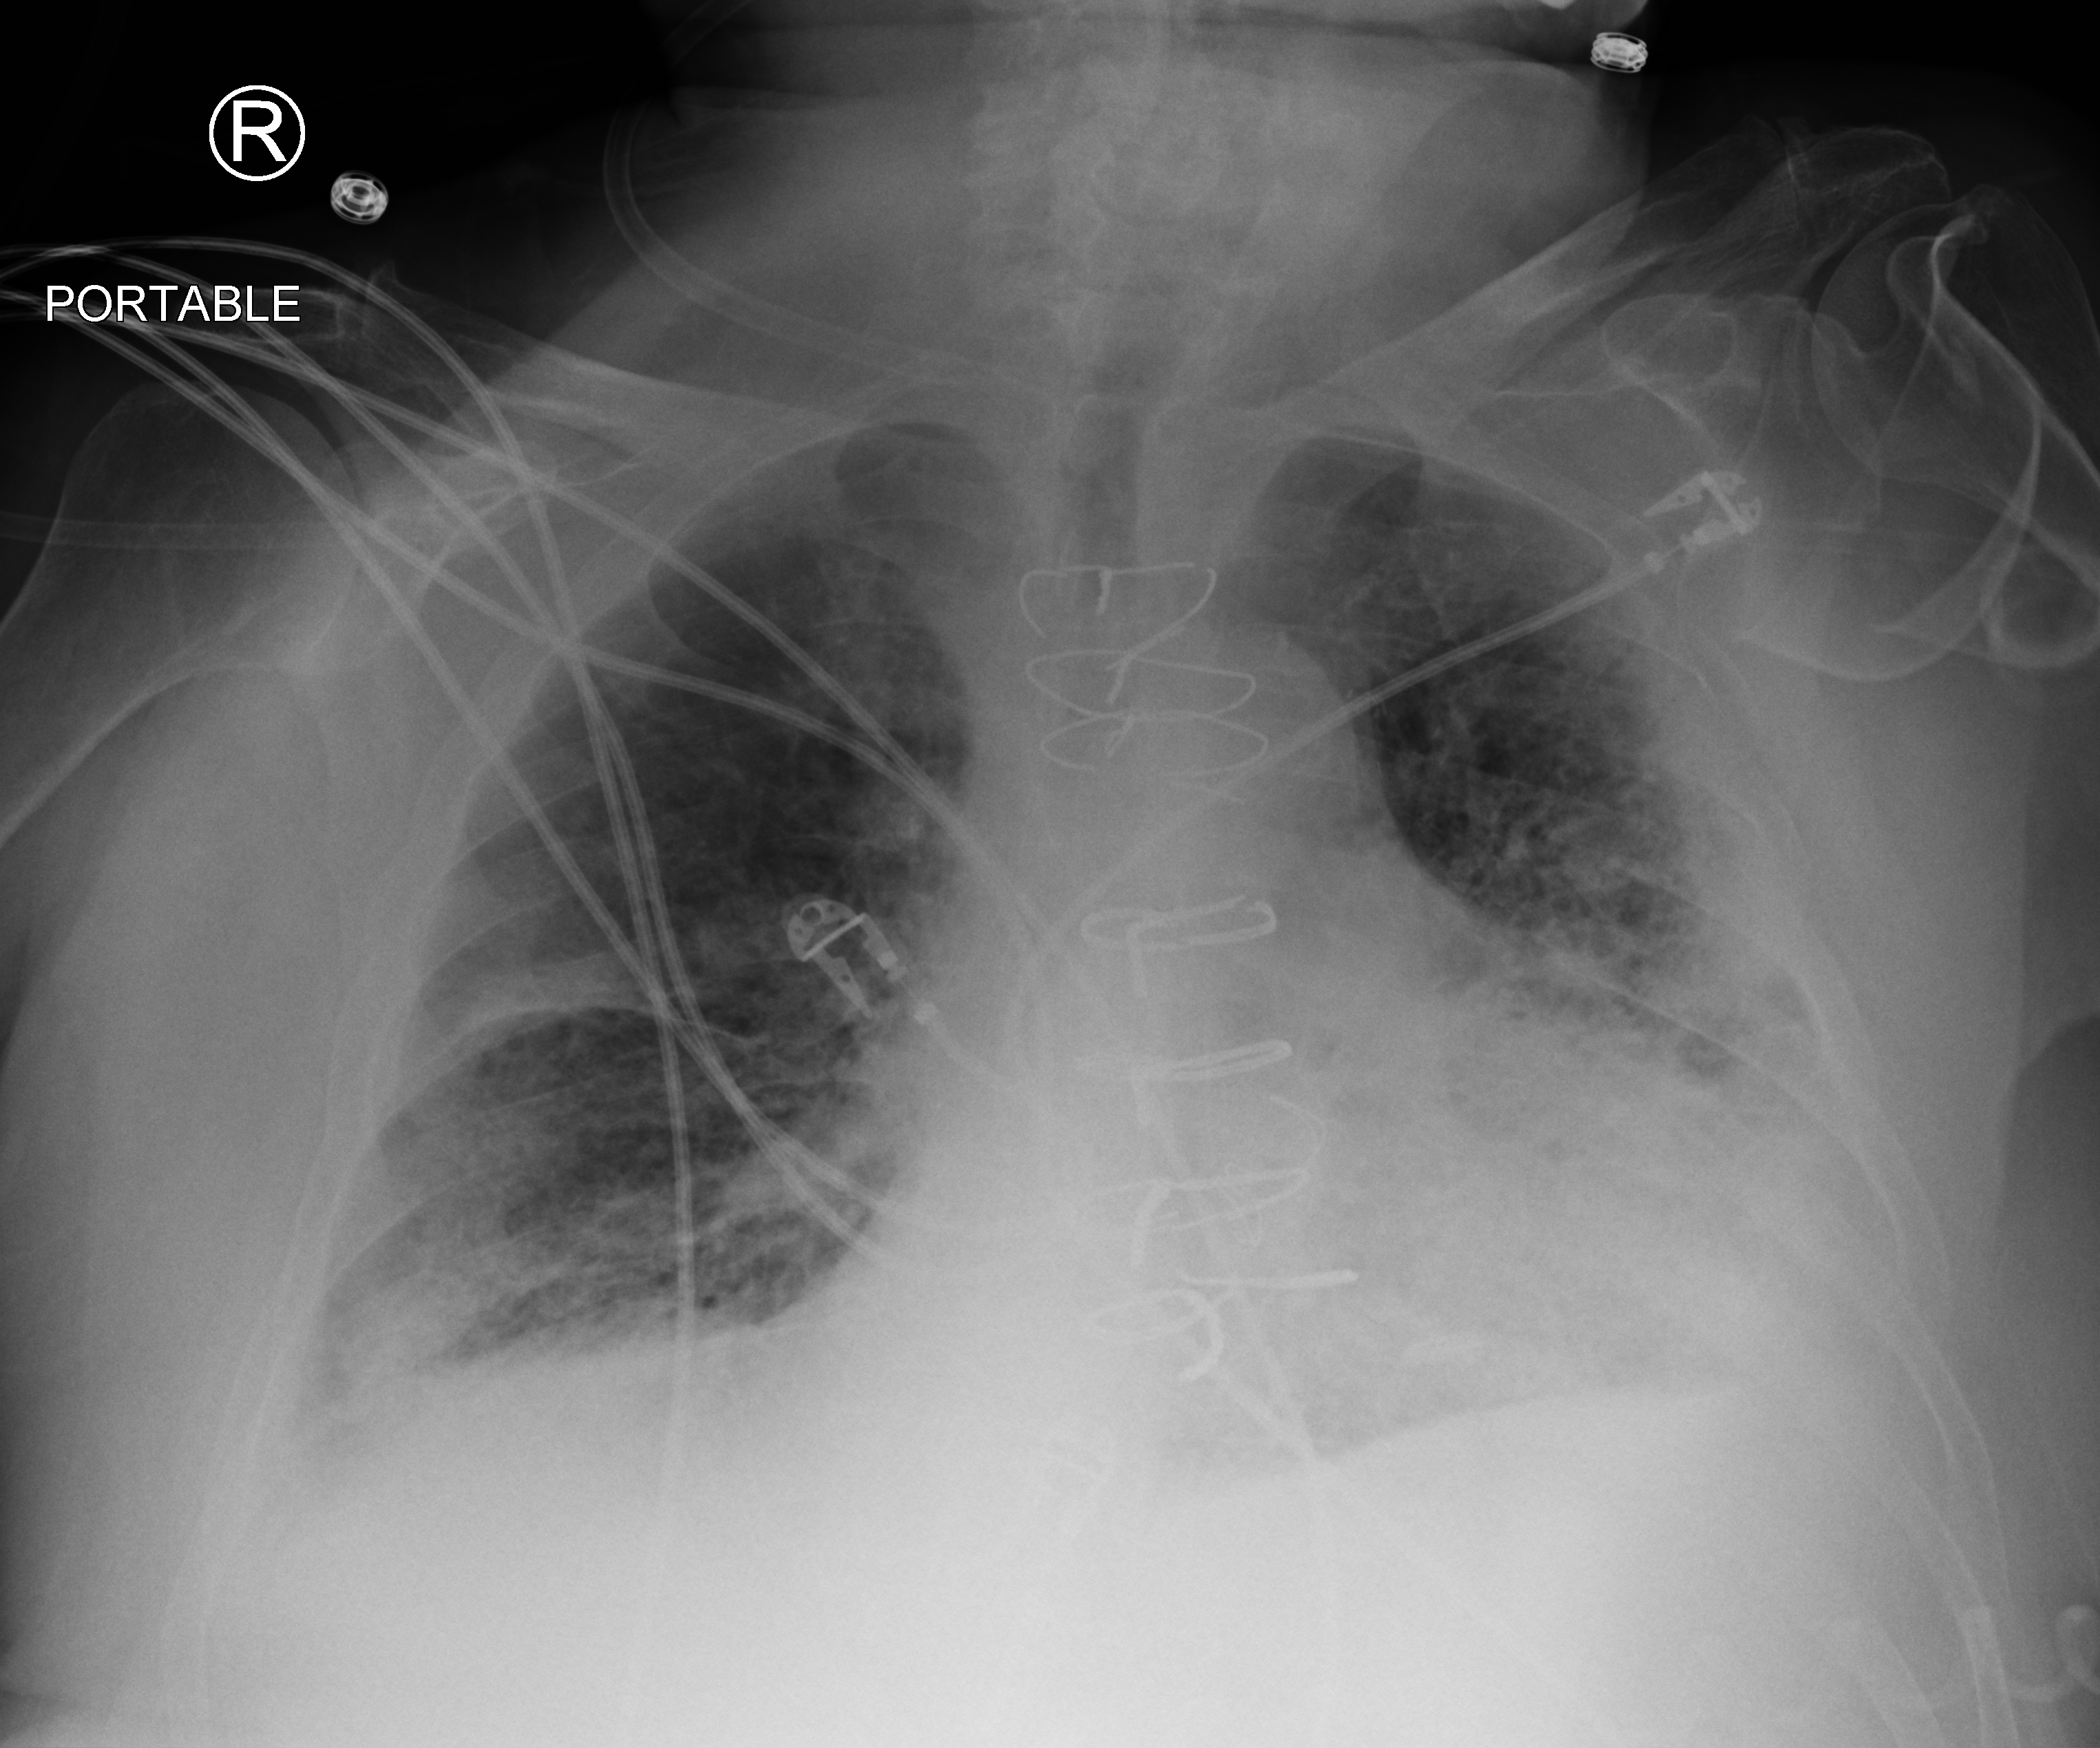
Bedside chest radiograph (computed radiography); anteroposterior (AP) projection. Patient hospitalised with COVID-19; male, aged 75–90 years.
From the hospital-stay record, not from the radiograph (when in the stay this image was taken is not recorded): admitted to intensive care during this hospital stay: no.